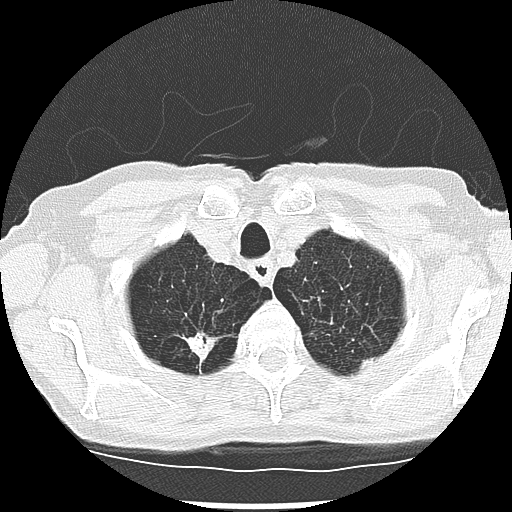
Low-dose screening chest CT, one axial slice; slice 239 of 265 in the series (ordered by position); reconstruction kernel LUNG; 120 kVp; lung window (W 1500 / L -600 HU); 512 × 512 image matrix, field of view 300 × 300 mm.
Structures marked on this image (manually delineated by an expert):
- lesion 2 (tumor, upper lobe of right lung): bounding box <185,332,216,362> (left, top, right, bottom; pixels)